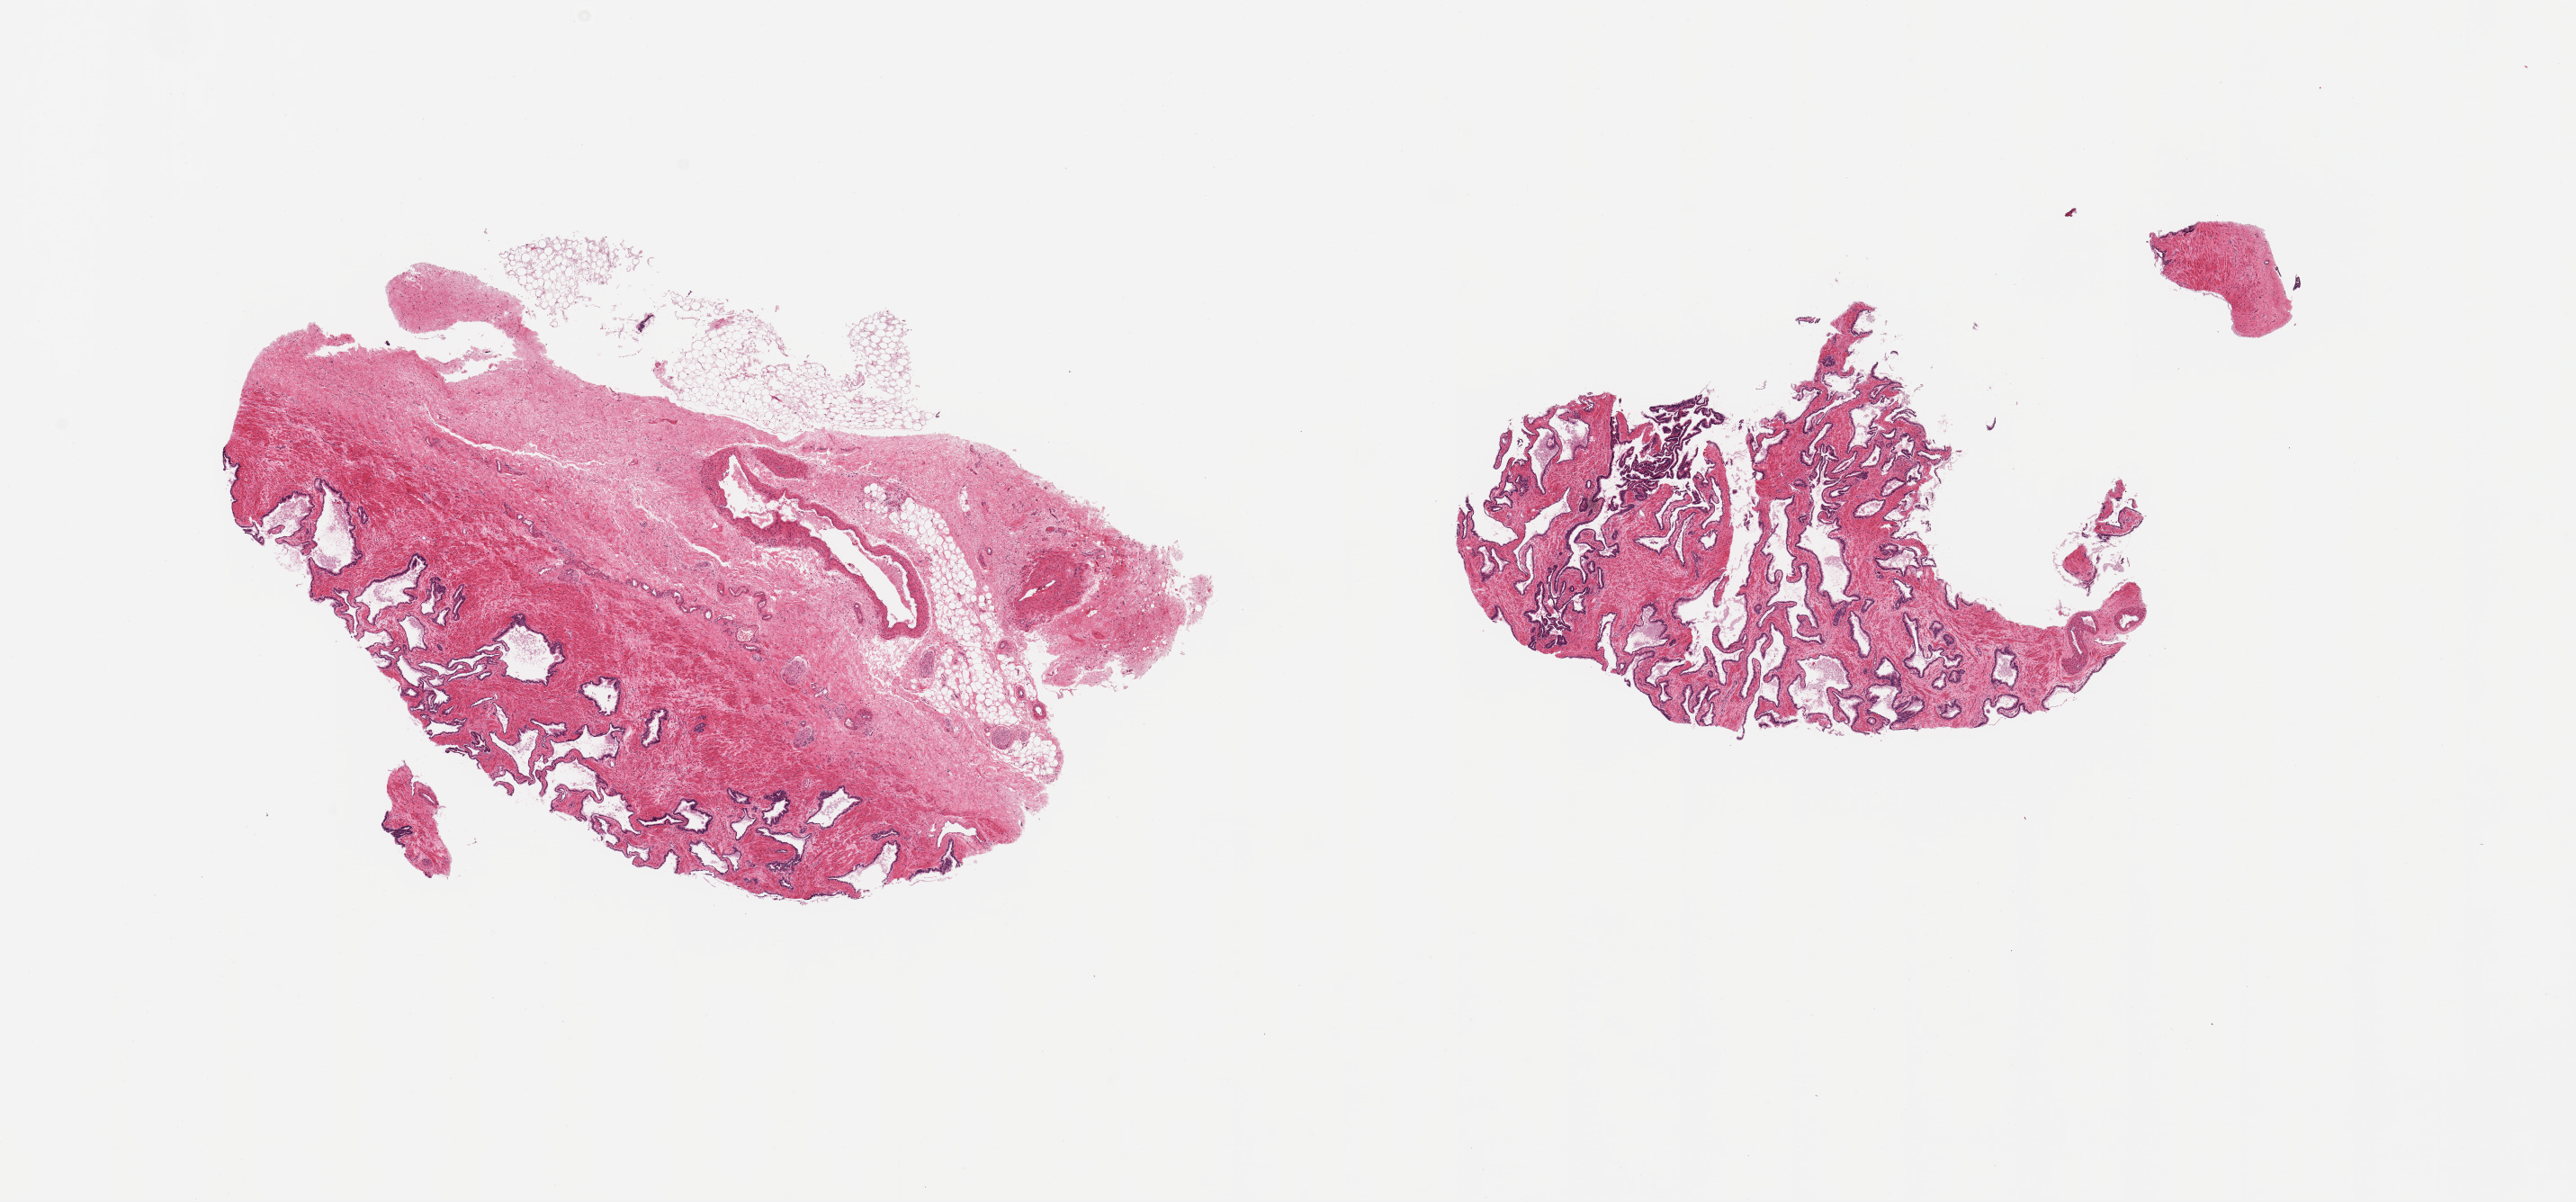
Digitized haematoxylin and eosin-stained section, whole scanned area (about 22.6 x 10.6 mm, acquisition: 20x scan) shown as a low-resolution overview; PAXgene-fixed, paraffin-embedded tissue; sampled site (target tissue): prostate; tissue donor sample.
• review note (as recorded): 2 pieces, glands well preserved; one aliquot is ~50% 'capsule' and fibrous tissue, glandular portion